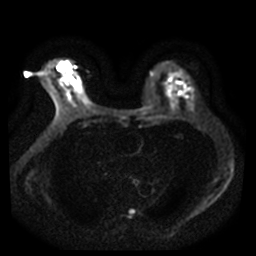
Breast MRI, one axial slice. Position 22 of 42 along the scan axis. Diffusion-weighted series; image 2 of 4 stored at this slice position (different b-values; order by instance number). 3 T. 256 × 256 image matrix, field of view 340 × 340 mm. Female patient.
Annotated regions visible in this slice (manually delineated by an expert):
- tumour on diffusion-weighted imaging: bounding box <58,63,71,71> (left, top, right, bottom; pixels)